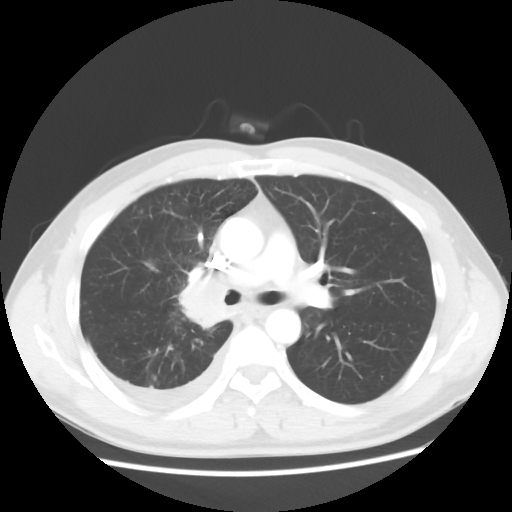
Chest CT, one axial slice; slice 33 of 56 in the series (ordered by position); reconstruction kernel STANDARD; 120 kVp; lung window (W 1500 / L -600 HU); 5 mm slice thickness; 512 × 512 image matrix, field of view 360 × 360 mm. Male patient, age 46 years. From the clinical record (not read from this slice): clinical TNM (as recorded): T2 N3 M1.
Structures marked on this image (rectangle marked by the reading radiologist):
- lung tumour (recorded histology: adenocarcinoma): box from (x=174, y=272) to (x=231, y=331) px